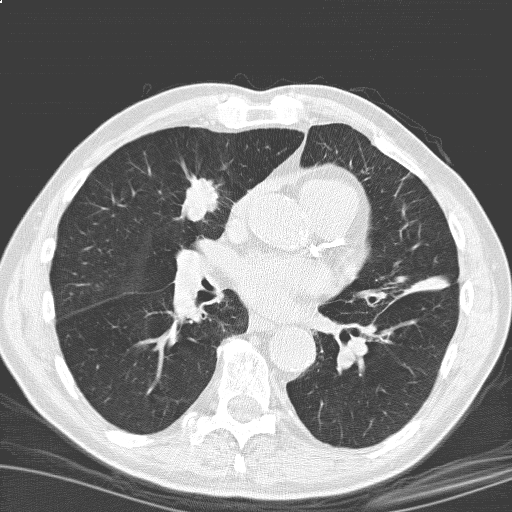
Low-dose screening chest CT, one axial slice. Lung window (W 1500 / L -600 HU). 3.2 mm slice thickness. 512 × 512 image matrix.
Outlined on this slice (outlined manually by an expert reader):
- lesion 1 (tumor, upper lobe of right lung): bounding box [x1, y1, x2, y2] px = [182, 178, 218, 221]